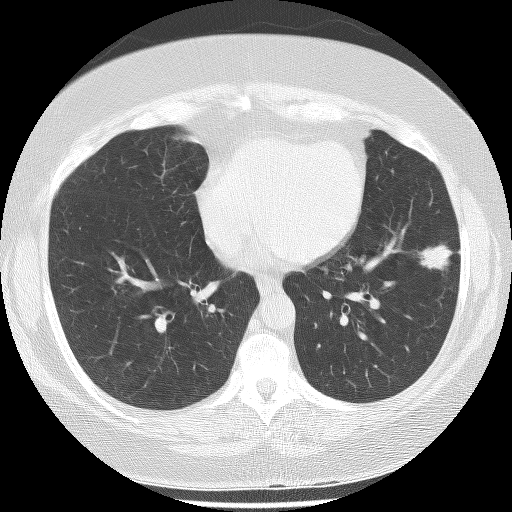
Low-dose screening chest CT, one axial slice. Position 104 of 233 along the scan axis. 120 kVp. Lung window (W 1500 / L -600 HU). 512 × 512 image matrix, field of view 340 × 340 mm.
Annotated regions visible in this slice (expert manual segmentation):
- lesion 1 (tumor, lower lobe of left lung): box from (x=418, y=243) to (x=454, y=275) px